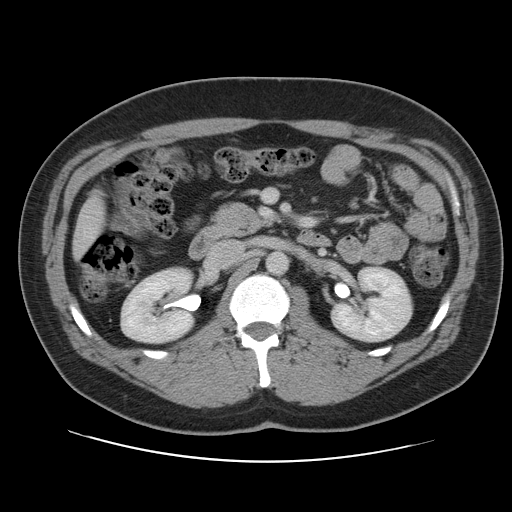
Contrast-enhanced abdominal CT, one axial slice; position 47 of 109 along the scan axis; 120 kVp; intravenous contrast given; soft-tissue window (W 400 / L 40 HU); 5 mm slice thickness; 512 × 512 image matrix, field of view 402 × 402 mm. Male patient, age 35 years. From the clinical record (not read from this slice): diagnosis: colorectal cancer liver metastases, imaged before liver resection; multiple liver metastases: yes; largest metastasis: 2.8 cm; disease in both lobes: yes.
Annotated regions visible in this slice (manually delineated by an expert):
- liver: bounding box (x1, y1, x2, y2) in pixels: (74, 197, 105, 255)
- planned liver remnant (the part of the liver to remain after resection): (74, 197, 105, 255)